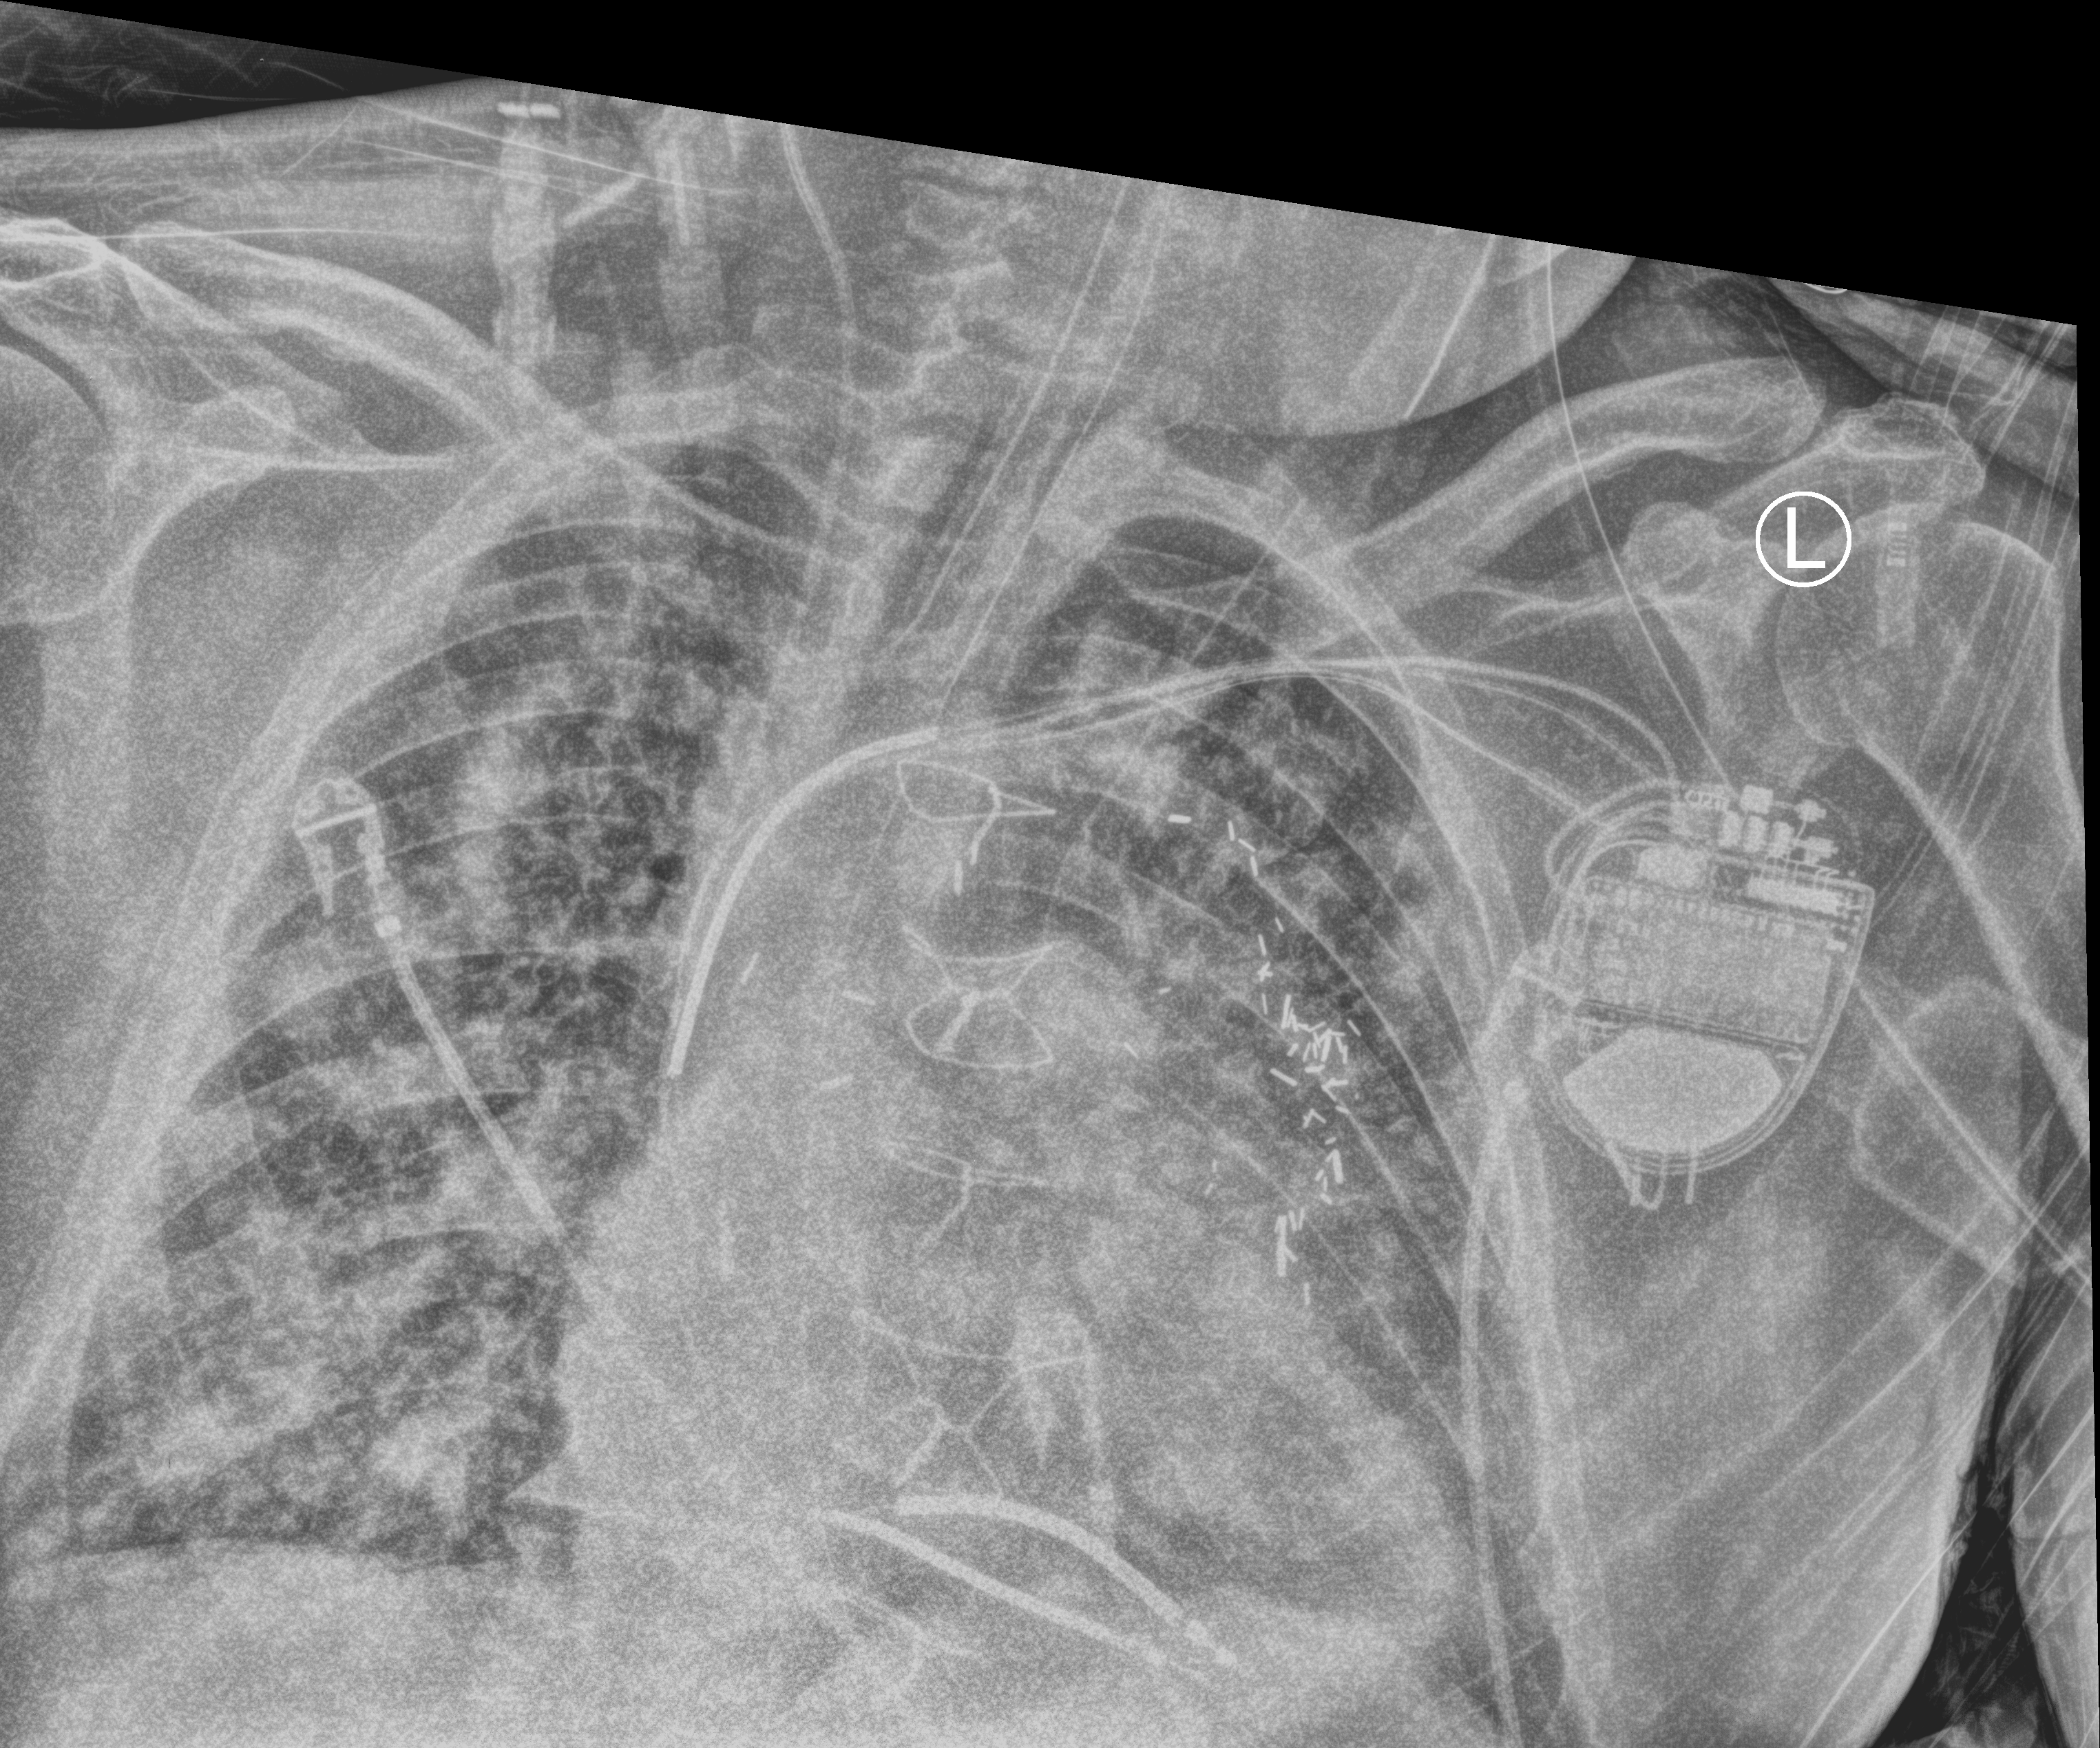
Bedside chest radiograph (computed radiography), anteroposterior (AP) projection. Male patient hospitalised with COVID-19, age 60–74 years.
From the hospital-stay record, not from the radiograph (when in the stay this image was taken is not recorded): diabetes (admission record): yes; mechanically ventilated during this hospital stay: yes.